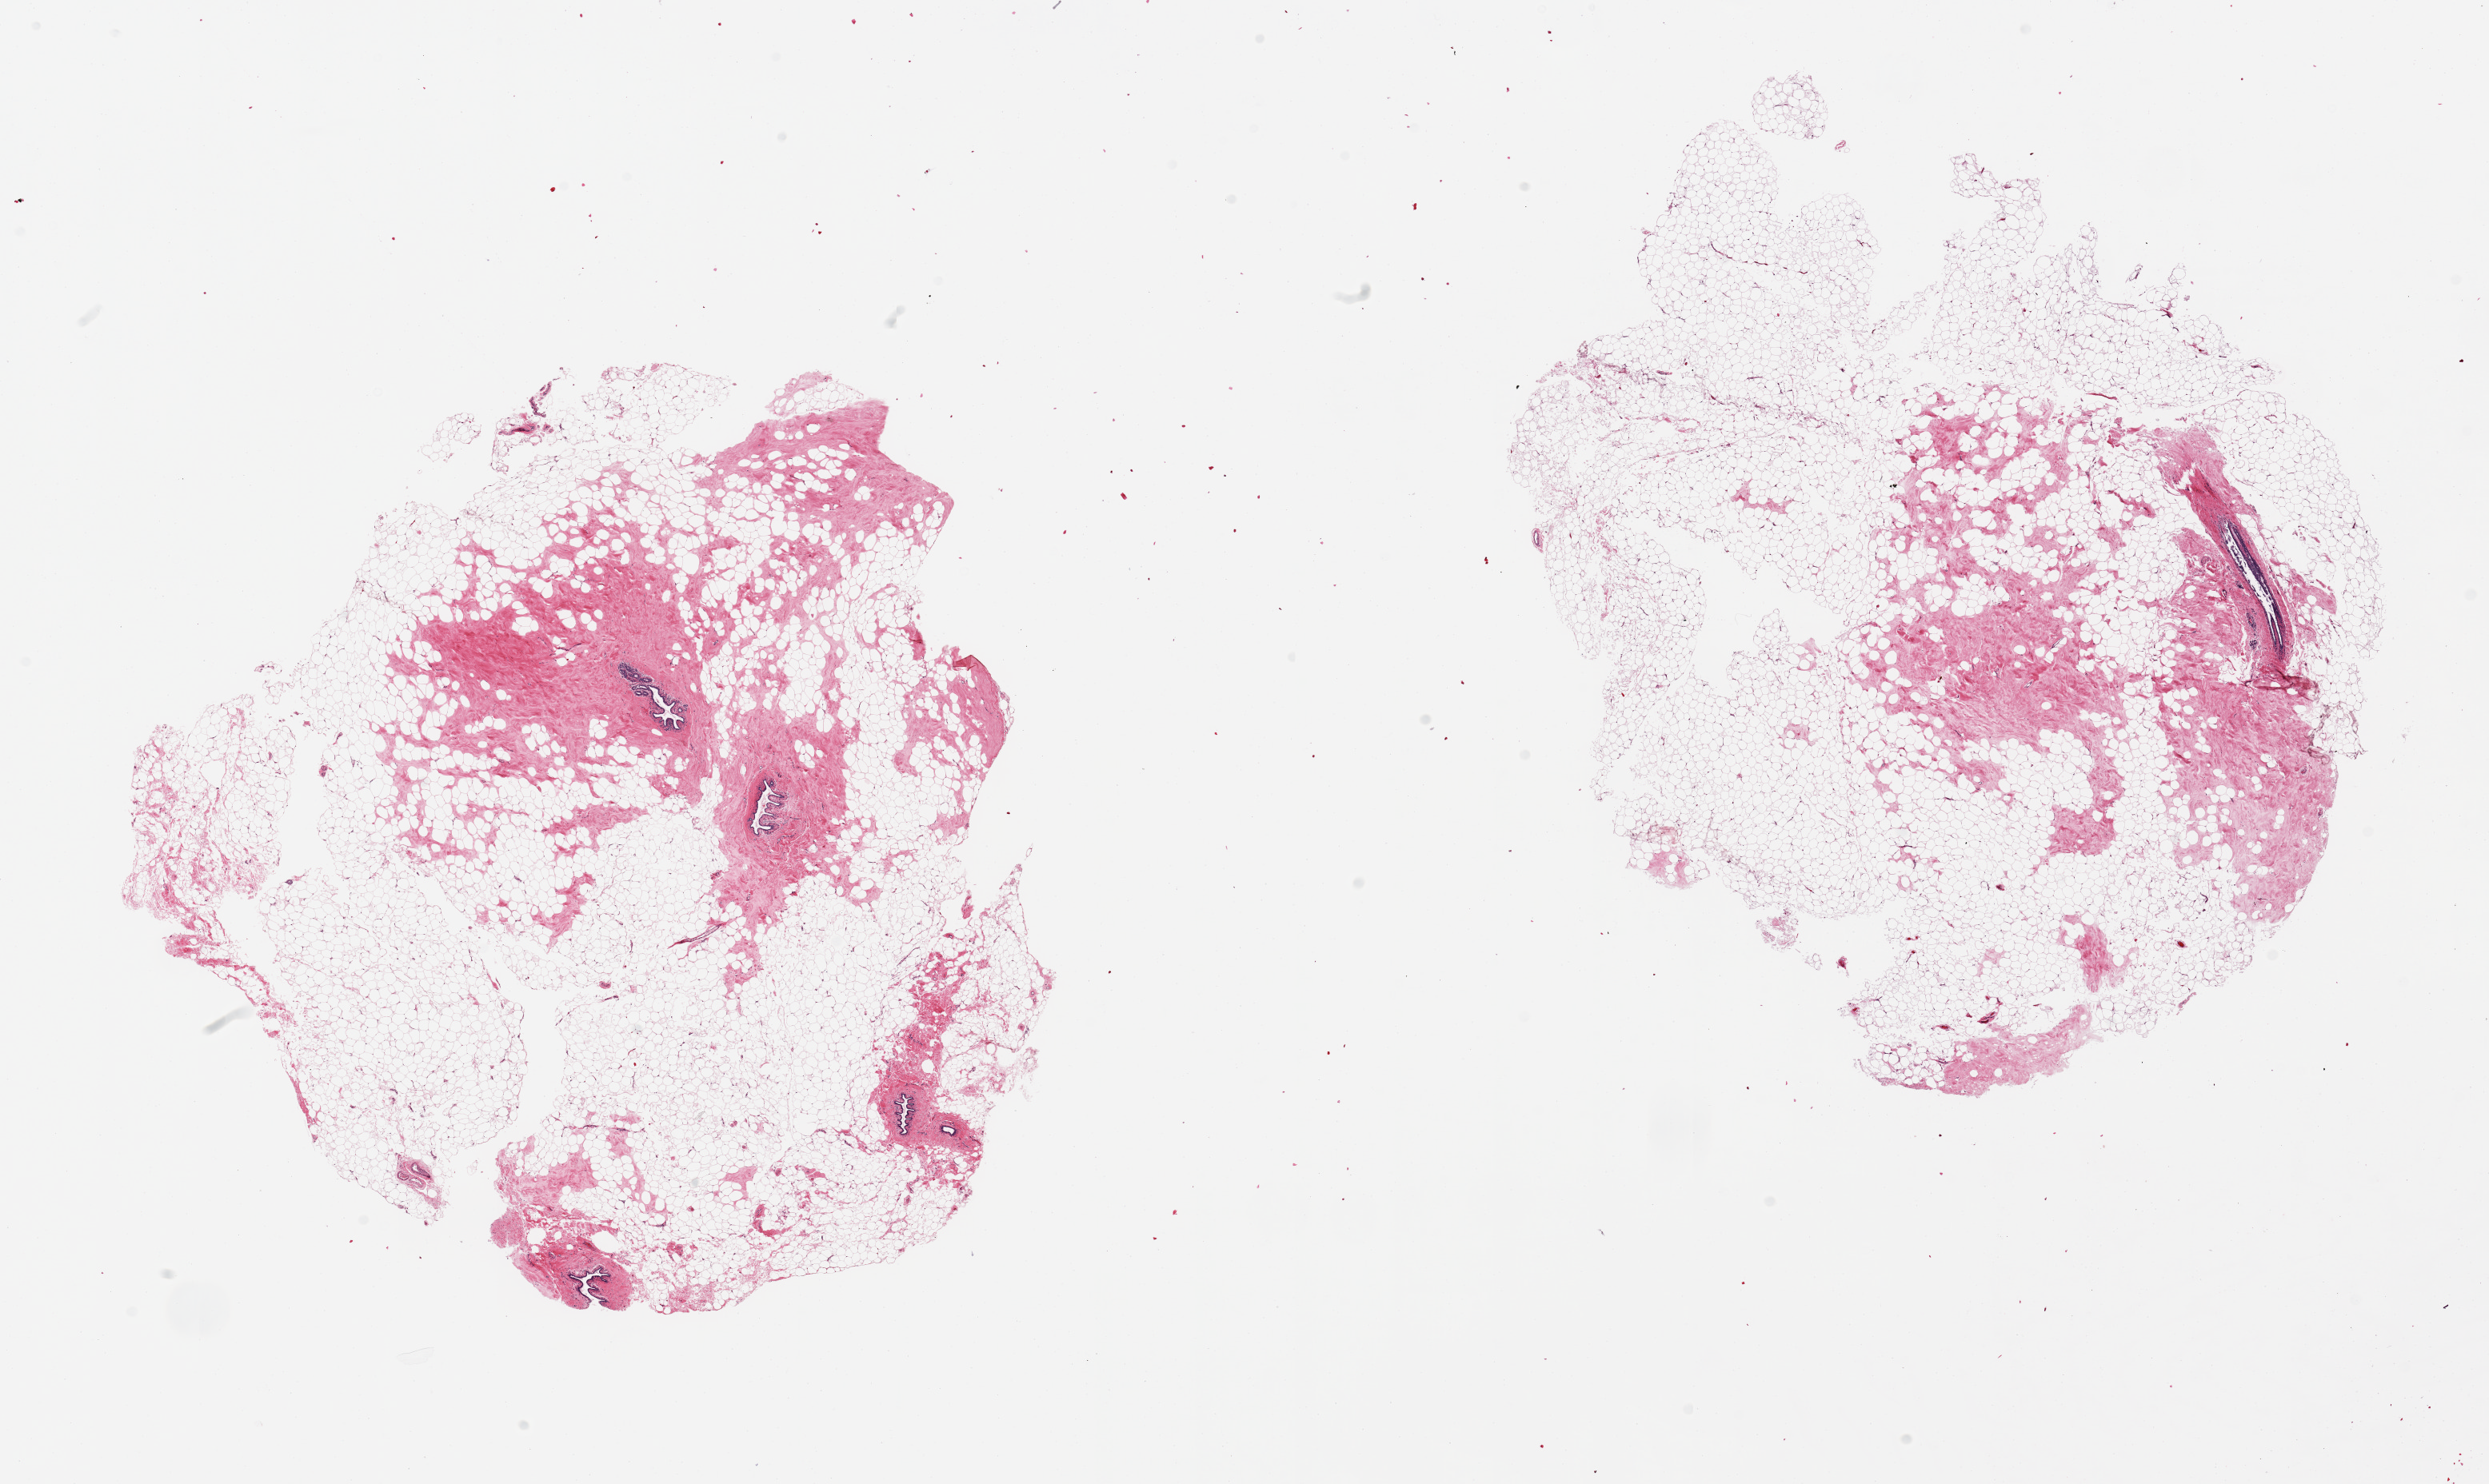
Digitized hematoxylin and eosin (H&E)-stained section — shown as a low-resolution overview of the whole scanned area (about 24.6 x 14.7 mm, from a 20x scan), PAXgene-fixed, paraffin-embedded tissue, sampled site (target tissue): breast, tissue donor sample. Female donor.
Reviewer comment on this tissue sample: 2 pieces; atrophic fatty tissue with a few ducts and fewer lobules.